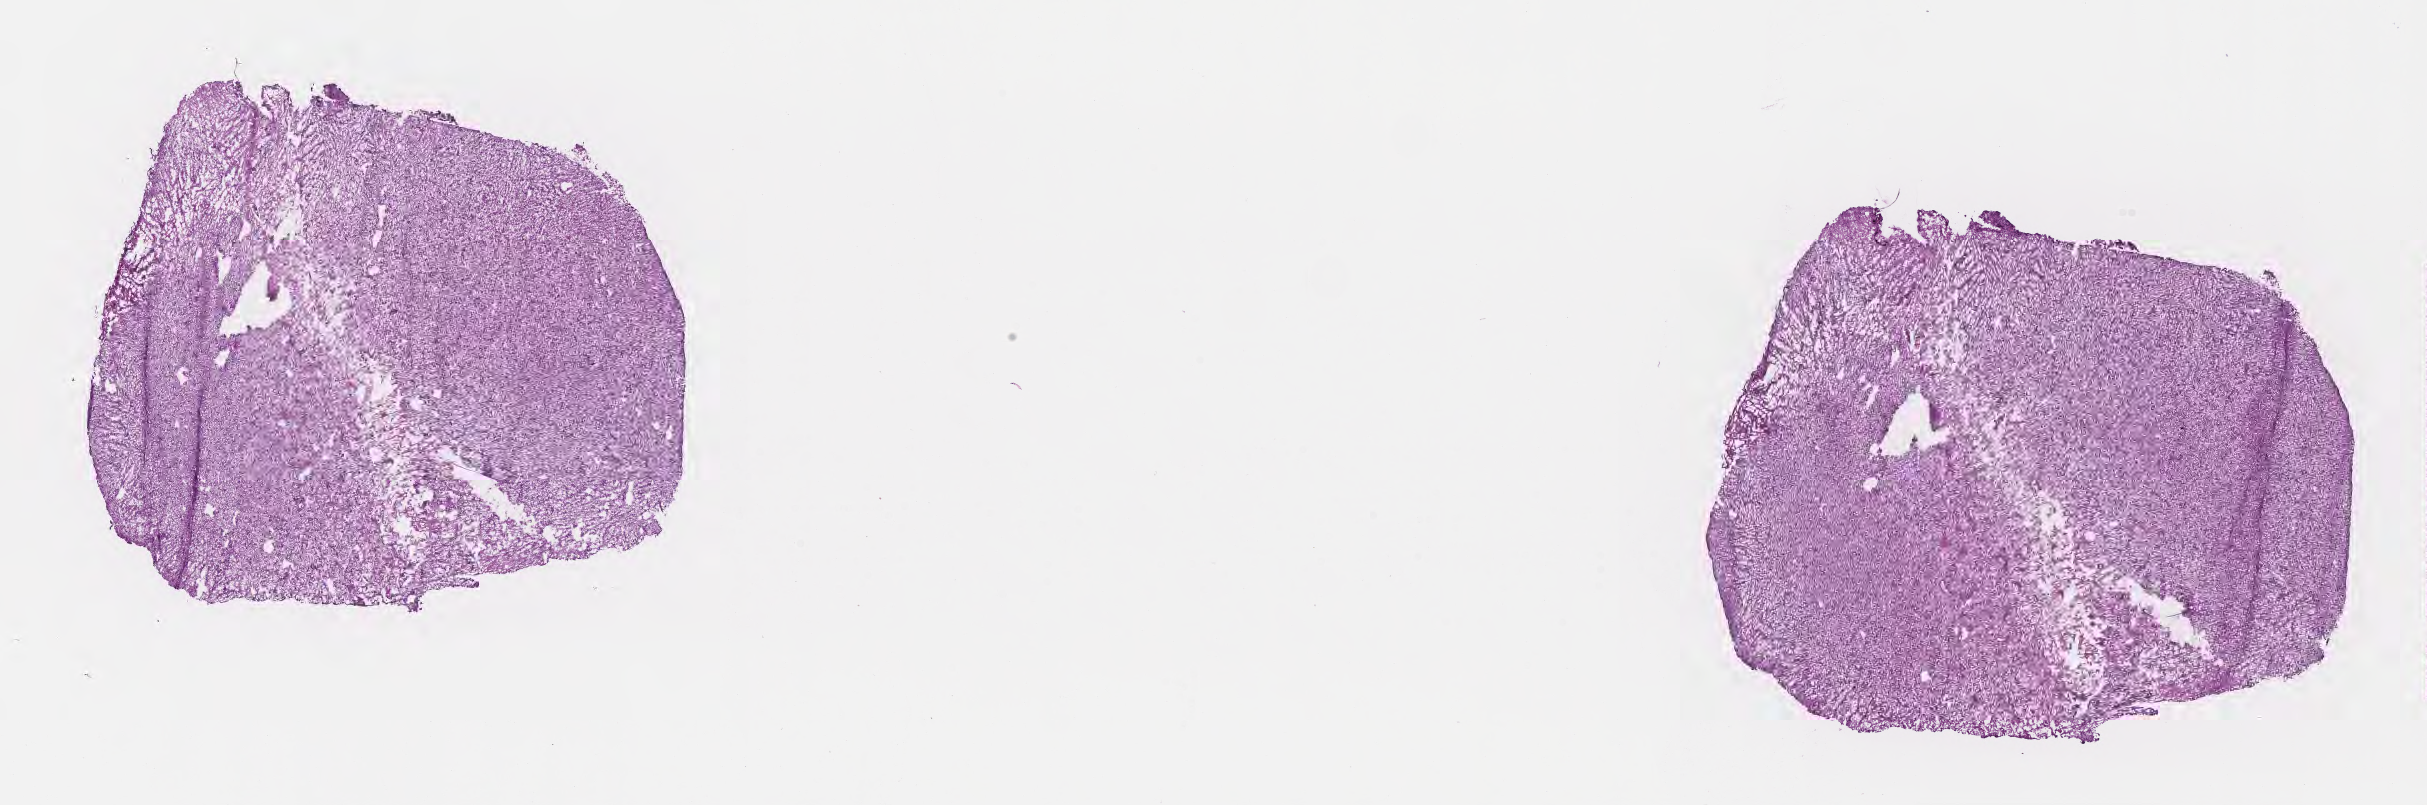
Whole-slide image, H&E stain — whole scanned area (about 19.6 x 6.5 mm) shown as a low-resolution overview, frozen section (snap frozen), primary tumor, anatomic site: brain. Male, age 58 years at initial diagnosis. Slide review estimates, as recorded: tumor cells 31%, tumor nuclei 54%, stromal cells 36%, necrosis 7%, normal cells 26%. Inflammatory infiltration, as recorded: lymphocyte infiltration 0%, monocyte infiltration 0%, neutrophil infiltration 0%.
Diagnosis: Glioblastoma, NOS.